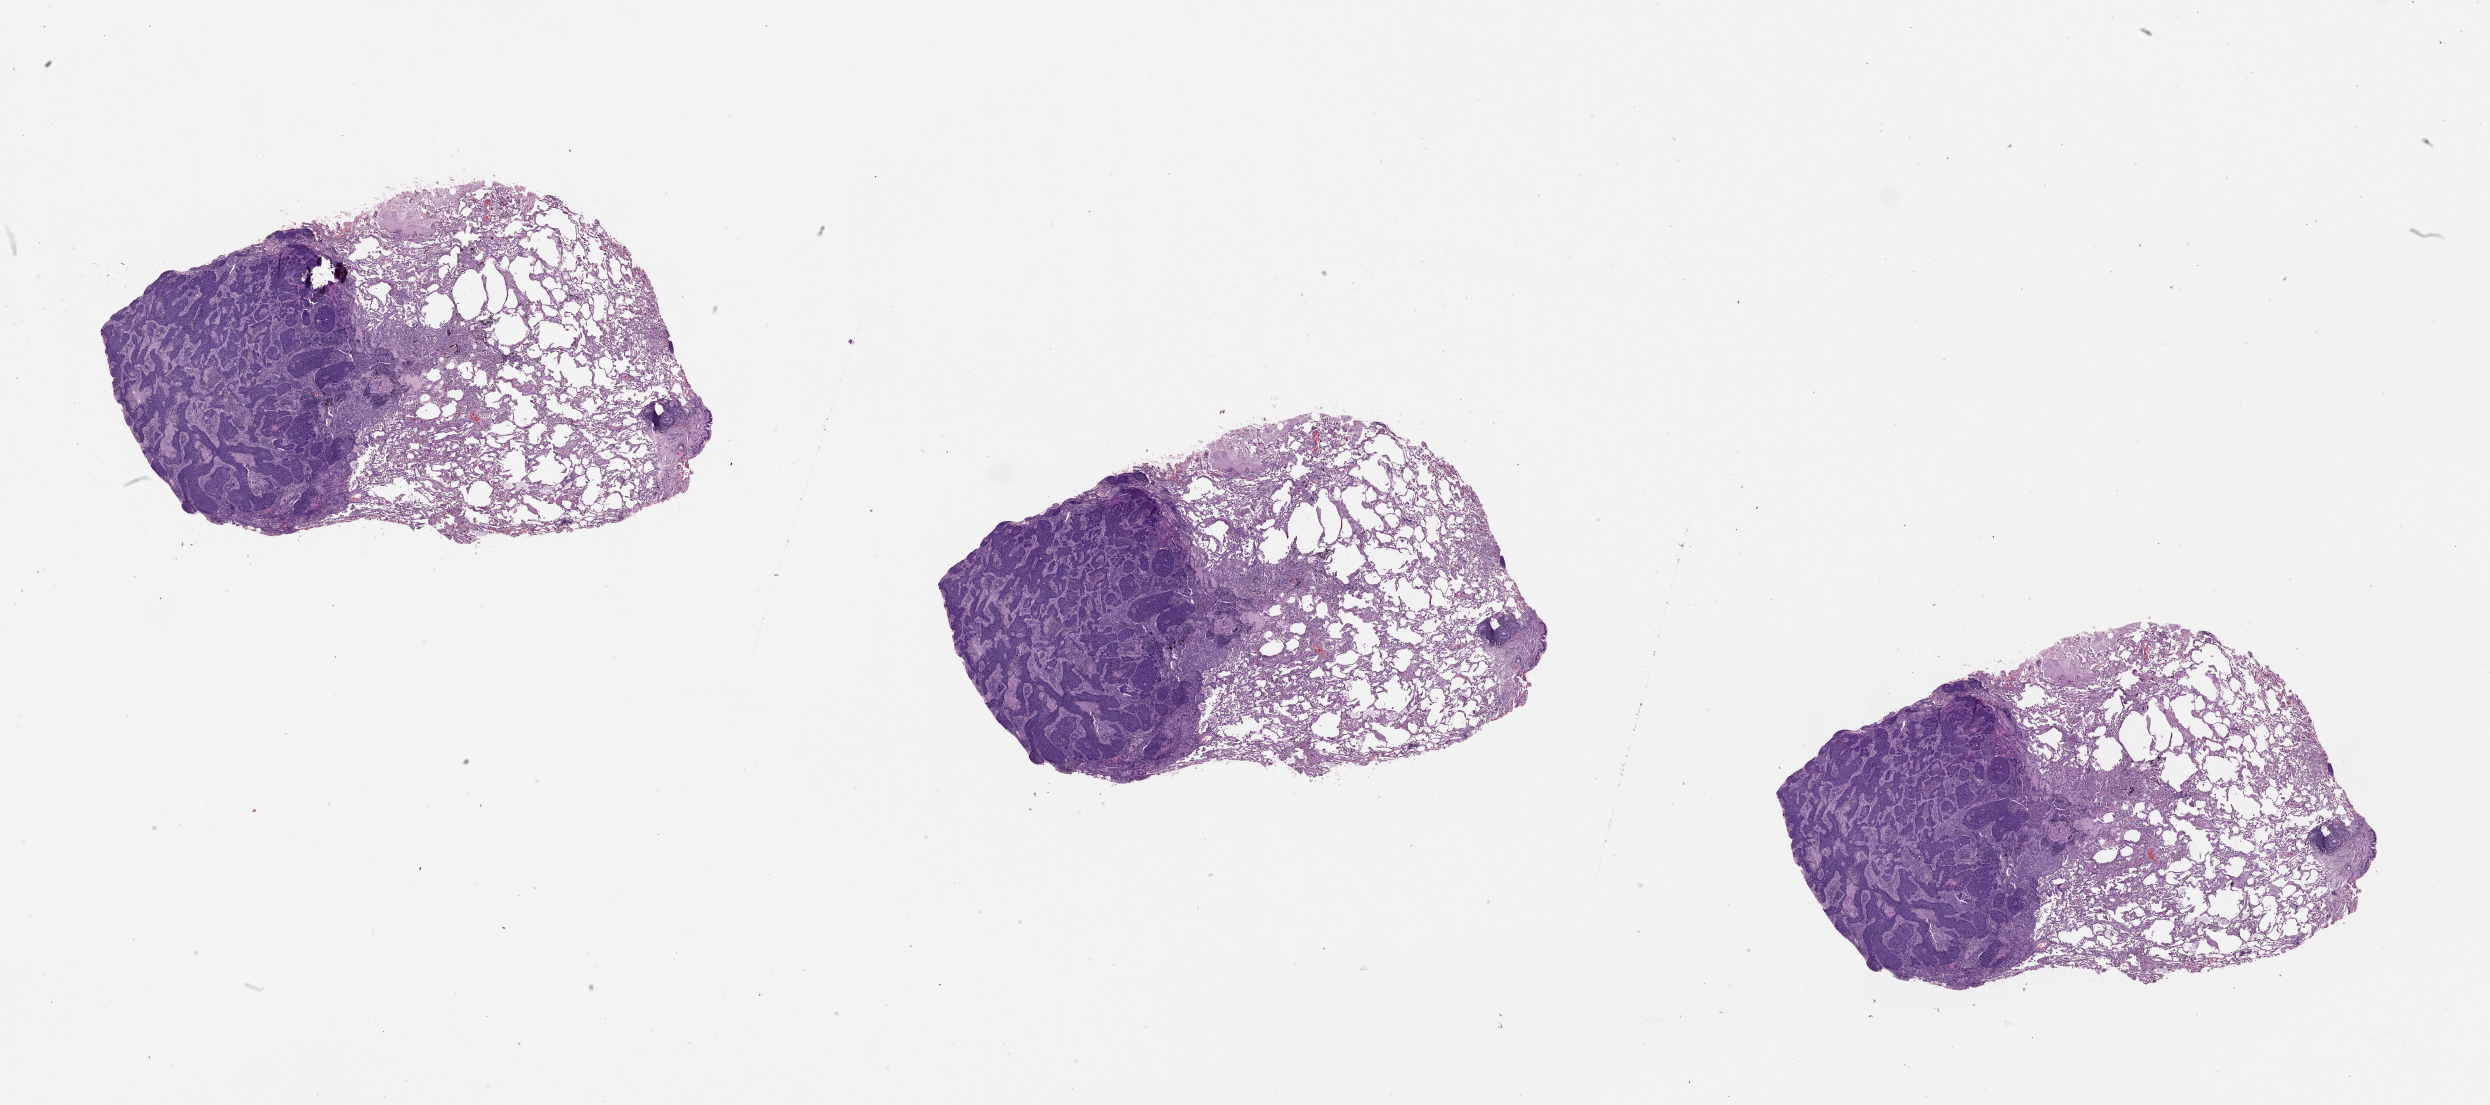
Digitized H&E-stained tissue section (whole slide), a low-resolution overview of the entire scanned area, about 40.1 x 17.8 mm (slide scanned at 20x); lung, tumour tissue. Female, 62 y/o.
Patient diagnosis (cohort enrolment): squamous cell carcinoma (lung).